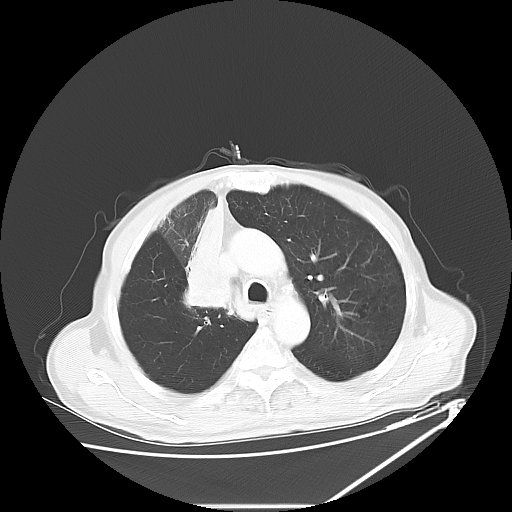
Chest CT, one axial slice. Slice 44 of 60 in the series (ordered by position). Reconstruction kernel LUNG. 120 kVp. Lung window (W 1500 / L -600 HU). 5 mm slice thickness. 512 × 512 image matrix. Patient: male, 73 years. Case-level facts recorded for this patient, not image findings: clinical TNM (as recorded): T2a N1 M0.
Structures marked on this image (rectangle marked by the reading radiologist):
- lung tumour (recorded histology: squamous cell carcinoma): bounding box (x1, y1, x2, y2) in pixels: (157, 195, 250, 321)